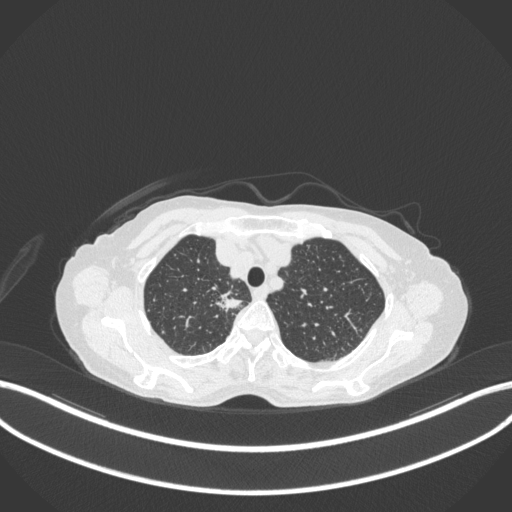
Chest CT, one axial slice; slice 307 of 363 in the series (ordered by position); 120 kVp; lung window (W 1500 / L -600 HU); 1 mm slice thickness; 512 × 512 image matrix, field of view 400 × 400 mm. Female patient, age 75 years. From the clinical record (not read from this slice): clinical TNM (as recorded): T1c N1 M1.
Structures marked on this image (rectangle marked by the reading radiologist):
- lung tumour (recorded histology: adenocarcinoma): bounding box (x1, y1, x2, y2) in pixels: (214, 287, 244, 319)